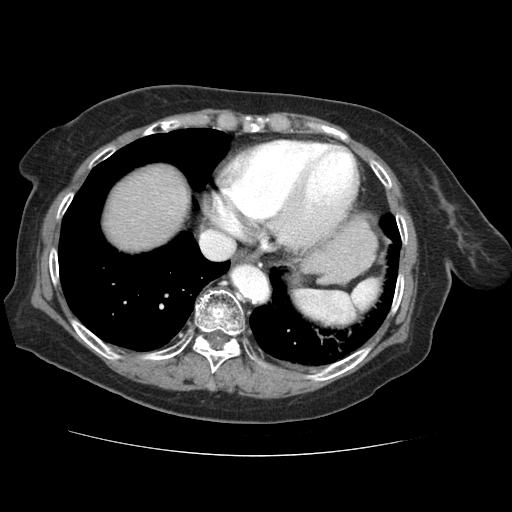
Contrast-enhanced abdominal CT (liver protocol), one axial slice. Slice 60 of 73 in the series (ordered by position). Reconstruction kernel STANDARD. 120 kVp. Soft-tissue window (W 400 / L 40 HU). 2.5 mm slice thickness. 512 × 512 image matrix, field of view 360 × 360 mm. Case-level facts recorded for this patient, not image findings: diagnosis: hepatocellular carcinoma (patient treated with transarterial chemoembolisation; whether this scan precedes or follows treatment is not stated here); TNM stage (as recorded): Stage-IVB; Child-Pugh class: A; tumour differentiation: well differentiated; tumour nodularity: uninodular.
Annotated regions visible in this slice (semi-automatic segmentation, software-assisted and operator-edited):
- liver parenchyma outside the tumour (the mass and vessels are separate outlines, so this box may not span the whole liver): bounding box <106,166,188,250> (left, top, right, bottom; pixels)